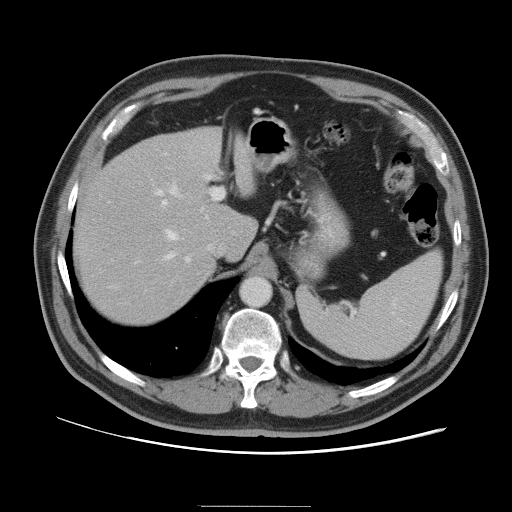
Contrast-enhanced abdominal CT, one axial slice; slice 72 of 105 in the series (ordered by position); intravenous contrast given; soft-tissue window (W 400 / L 40 HU); 5 mm slice thickness; 512 × 512 image matrix. Male patient, age 64 years. From the clinical record (not read from this slice): diagnosis: colorectal cancer liver metastases, imaged before liver resection; multiple liver metastases: yes; largest metastasis: 3 cm.
Outlined on this slice (outlined manually by an expert reader):
- hepatic veins: bounding box <166,185,182,259> (left, top, right, bottom; pixels)
- liver: <75,128,255,325>
- planned liver remnant (the part of the liver to remain after resection): <74,143,255,325>
- portal vein (with intrahepatic branches): <155,174,224,263>